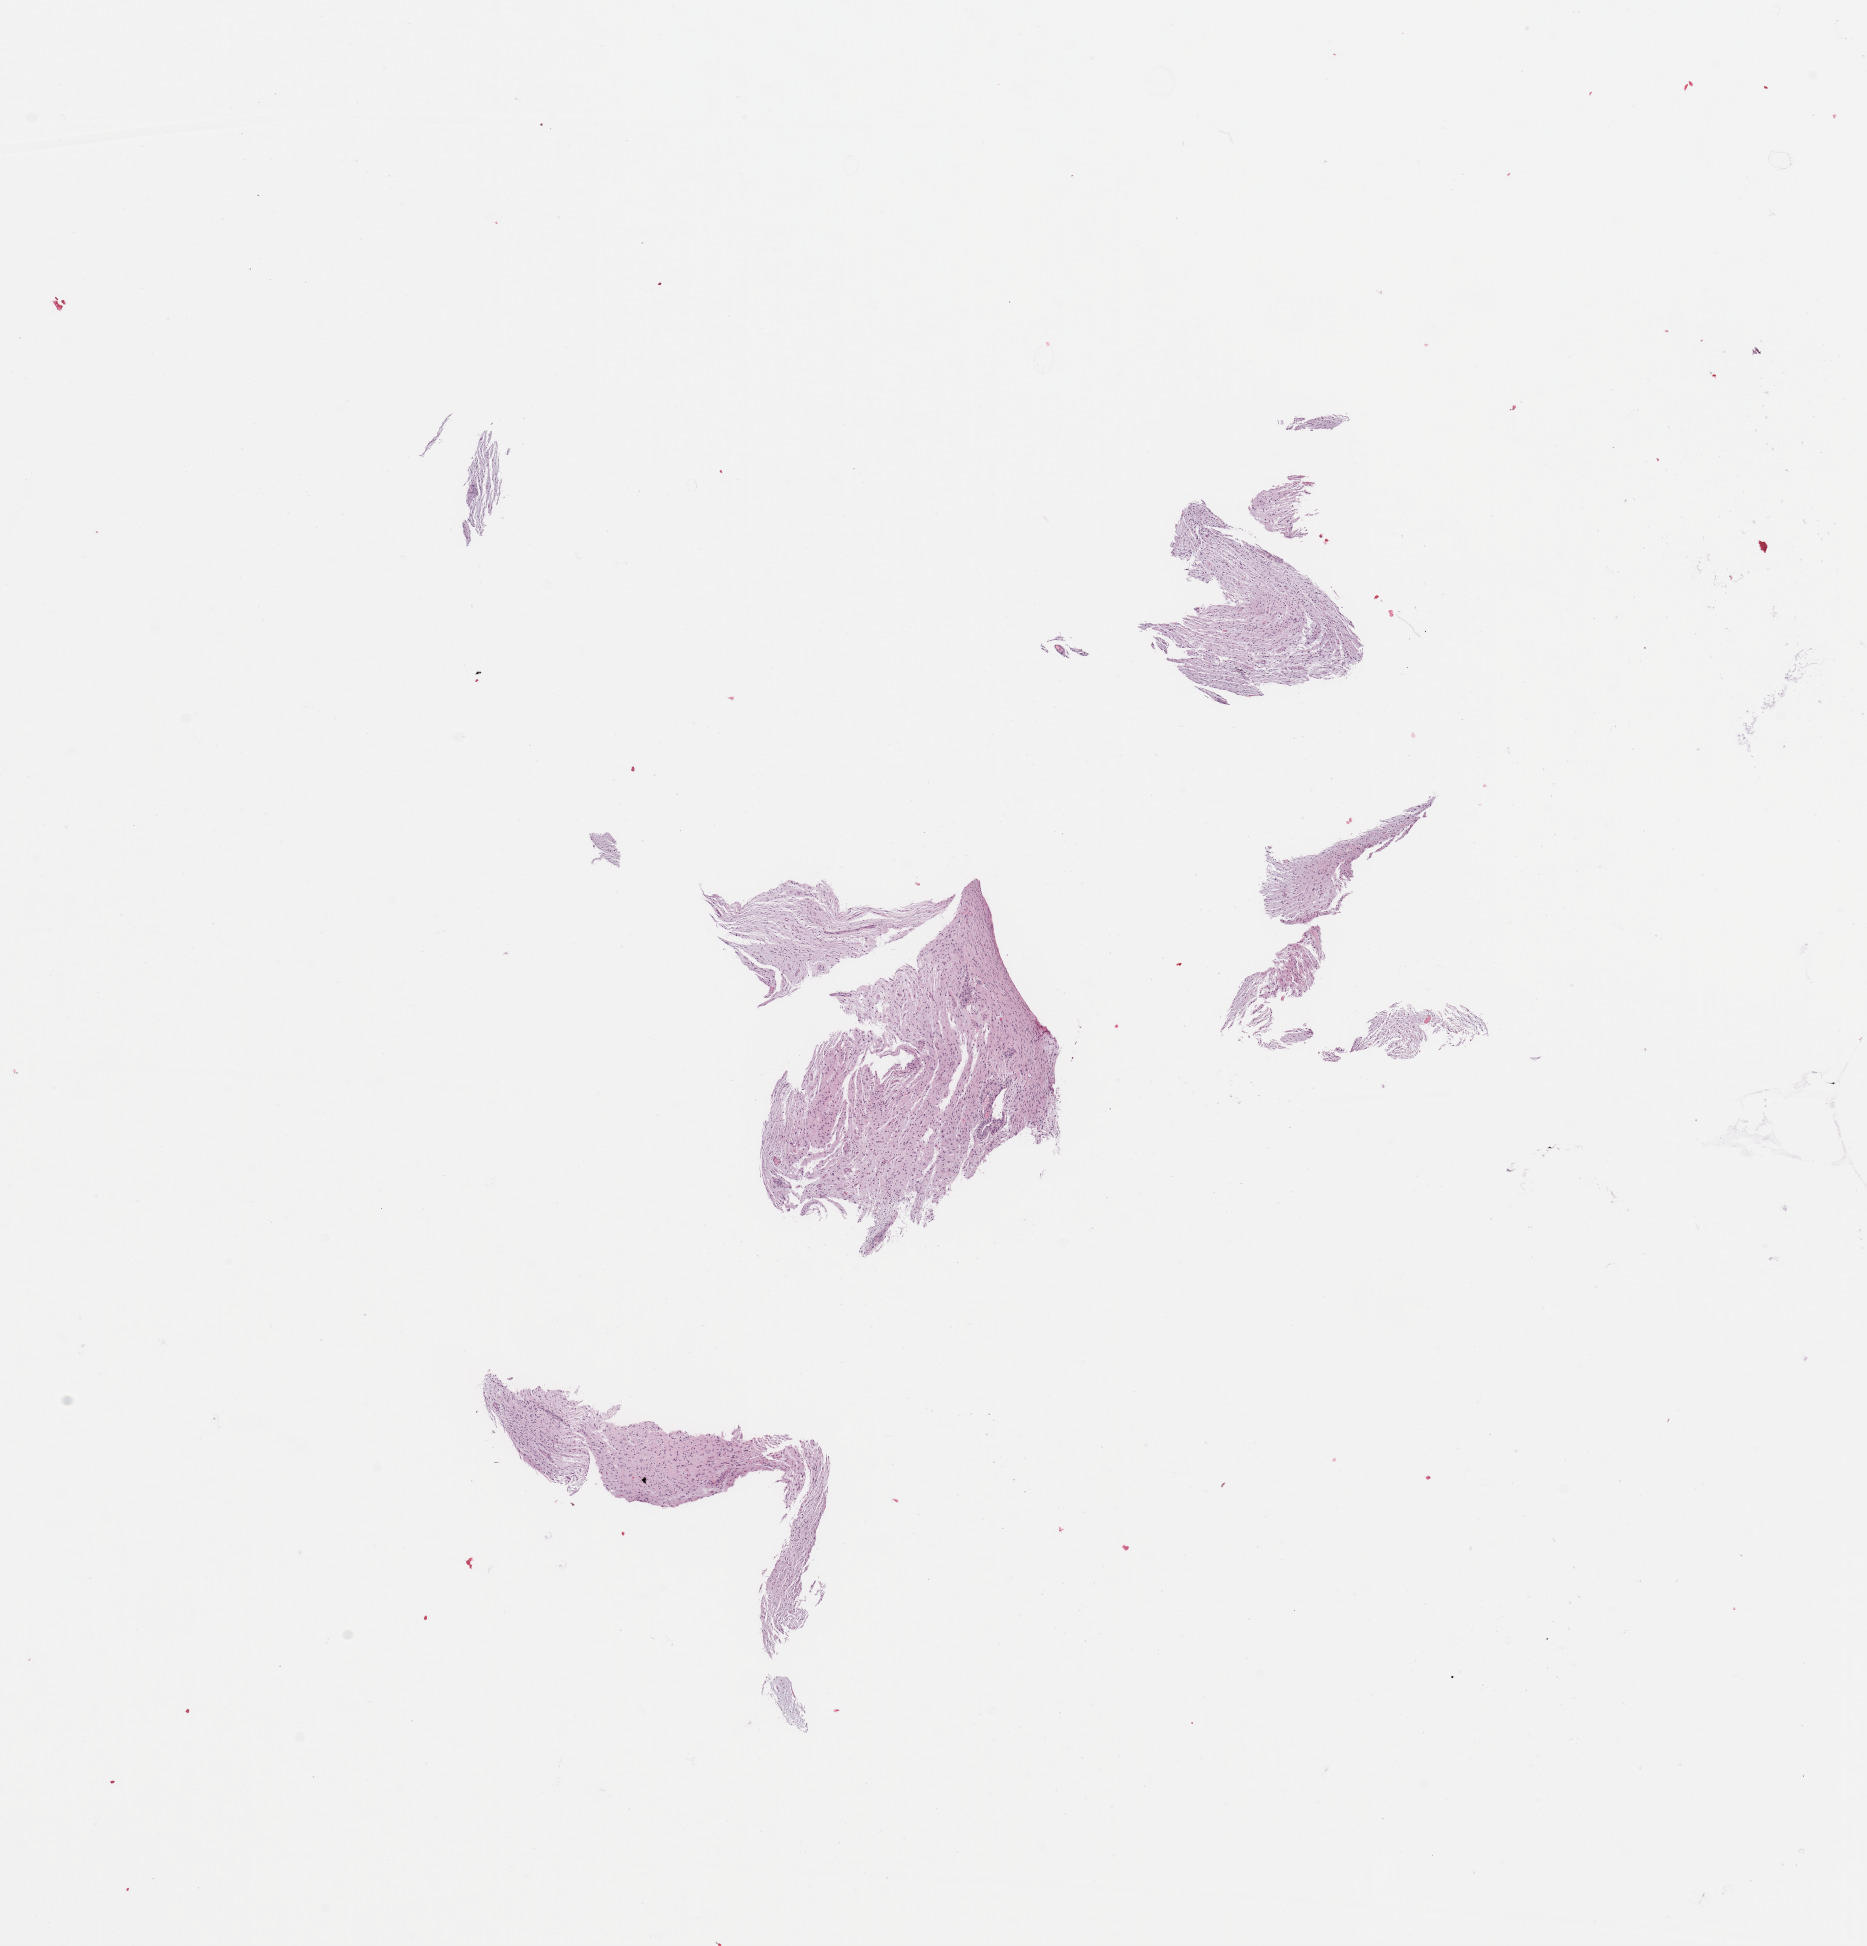
Hematoxylin and eosin (H&E) stained whole-slide image, shown as a low-resolution overview of the whole scanned area (about 14.8 x 15.4 mm, slide scanned at 20x). Tumour tissue sample, sampled site: frontal lobe. Female, 57 y/o. Pathologist review of this section (percent, as recorded): tumour nuclei 75%, necrosis 5%.
Histologic diagnosis: Glioblastoma.